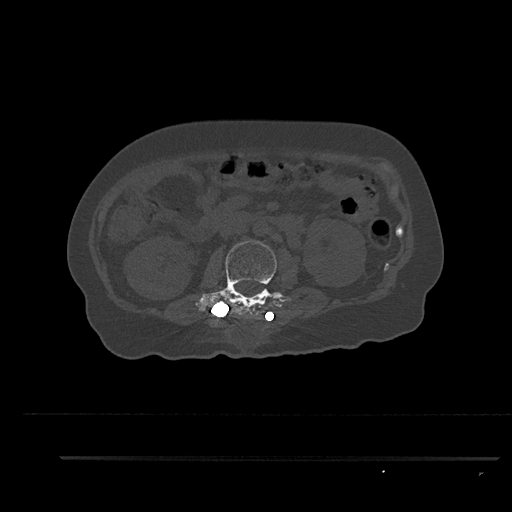
CT including the spine, one axial slice. Position 151 of 797 along the scan axis. Reconstruction kernel Br40s/3. Bone window (W 1800 / L 400 HU). 0.5 mm slice thickness. 512 × 512 image matrix, field of view 408 × 408 mm. Female patient, age 44 years. From the clinical record (not read from this slice): primary cancer: renal.
Annotated regions visible in this slice (semi-automatically segmented with operator editing):
- L2 vertebra: bounding box (x1, y1, x2, y2) in pixels: (195, 239, 281, 319)